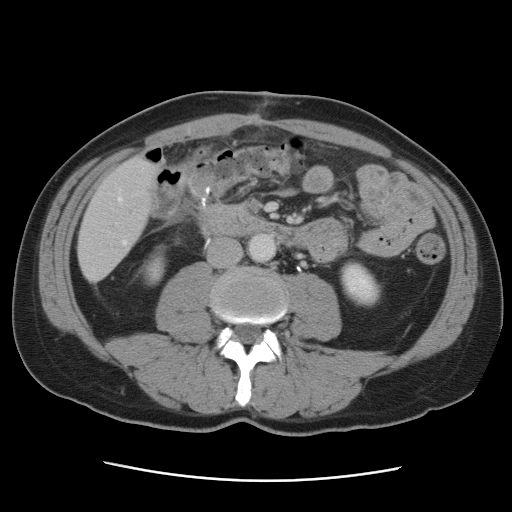
Contrast-enhanced abdominal CT, one axial slice; slice 17 of 89 in the series (ordered by position); 120 kVp; soft-tissue window (W 400 / L 40 HU); 512 × 512 image matrix, field of view 366 × 366 mm. Male patient, age 59 years. From the clinical record (not read from this slice): diagnosis: colorectal cancer liver metastases, imaged before liver resection; multiple liver metastases: yes; largest metastasis: 0.6 cm; disease in both lobes: yes.
Structures marked on this image (expert manual segmentation):
- hepatic veins: box from (x=118, y=190) to (x=127, y=244) px
- liver: (x=79, y=157)–(x=159, y=281)
- planned liver remnant (the part of the liver to remain after resection): (x=79, y=156)–(x=159, y=256)